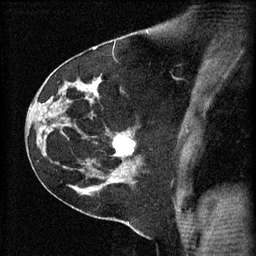
Breast MRI (dynamic contrast-enhanced), one sagittal slice; position 38 of 60 along the scan axis; 3 images stored at this slice position (order not interpretable as contrast timing); 1.5 T; TE 4.2 ms, TR 11 ms; 2 mm slice thickness; 256 × 256 image matrix, field of view 180 × 180 mm. Patient: female, 45 years.
Structures marked on this image (semi-automatic segmentation, software-assisted and operator-edited):
- analysis volume of interest (the breast-tissue region the enhancement analysis was run in; not a lesion): bounding box <110,130,143,171> (left, top, right, bottom; pixels)
- tumour enhancement mask (voxels above the 70 % enhancement threshold inside the analysis volume of interest): <114,136,135,157>